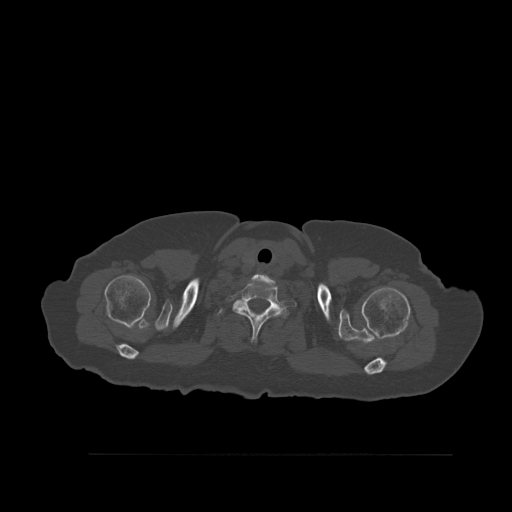
CT including the spine, one axial slice; position 452 of 527 along the scan axis; bone window (W 1800 / L 400 HU); 512 × 512 image matrix. Female patient, age 73 years. From the clinical record (not read from this slice): primary cancer: breast; vertebrae with lytic lesions (as recorded): L2.
Annotated regions visible in this slice (semi-automatic segmentation, software-assisted and operator-edited):
- T1 vertebra: bounding box (x1, y1, x2, y2) in pixels: (217, 308, 224, 317)